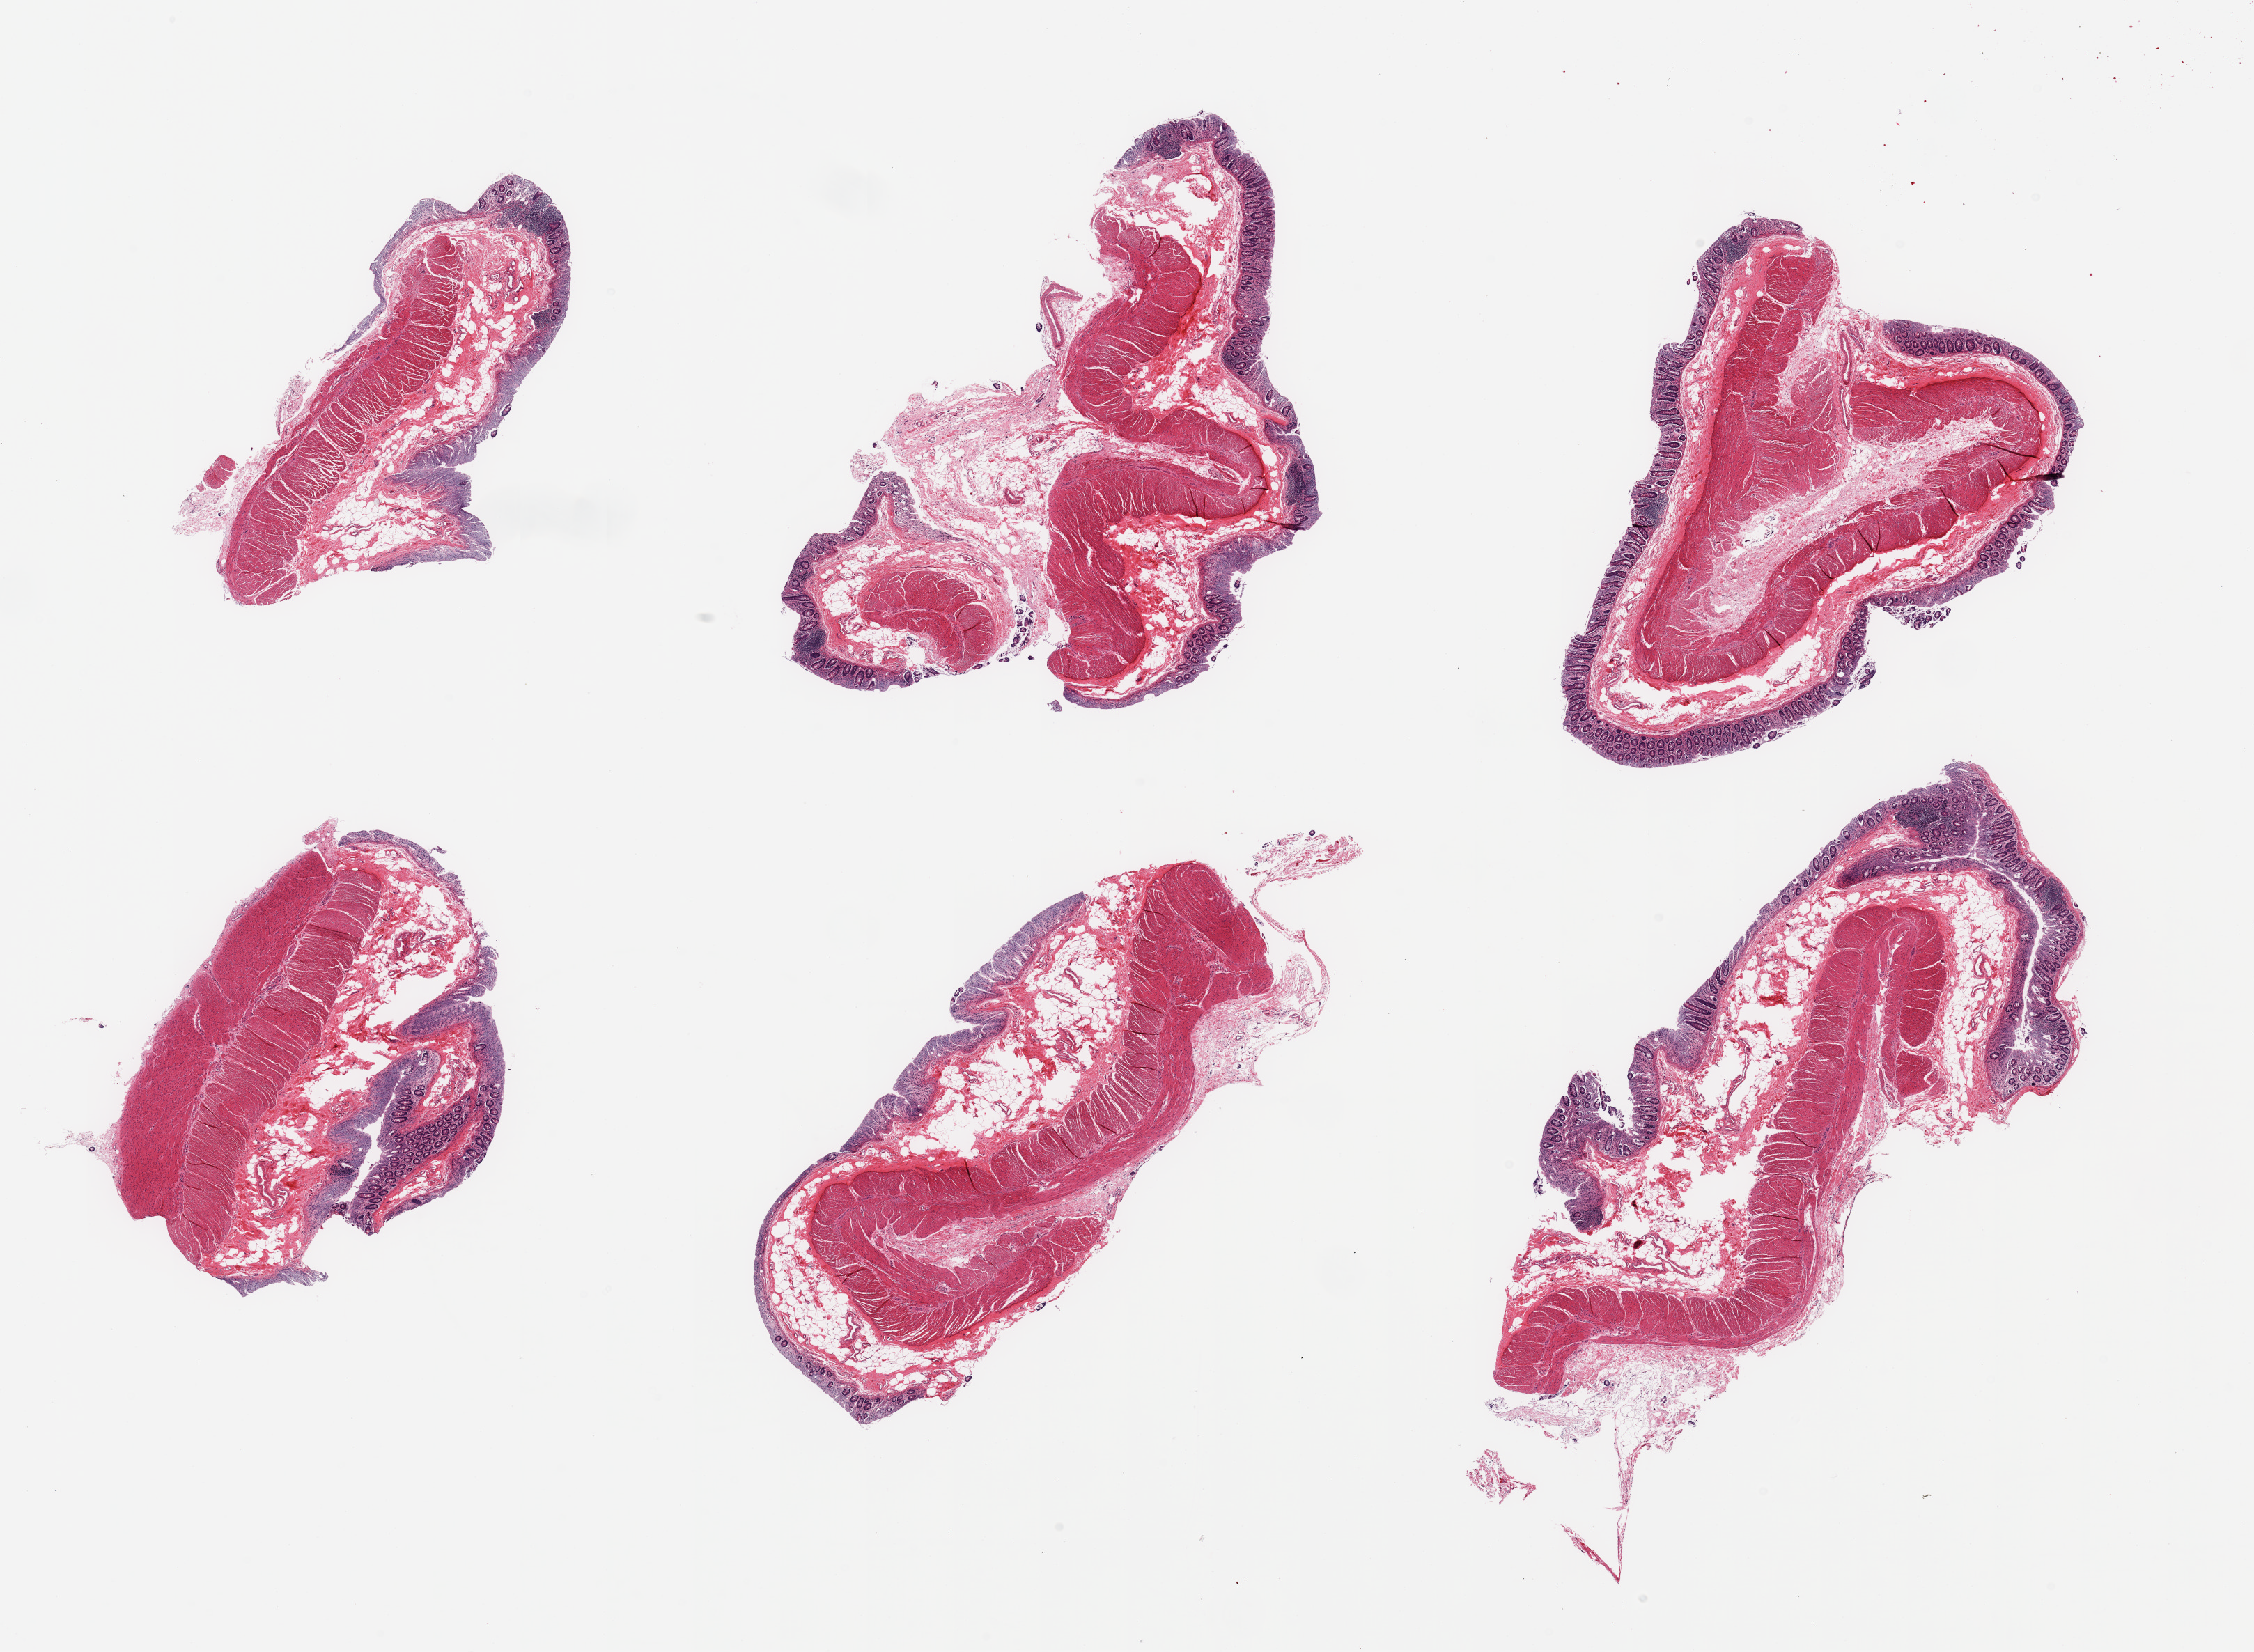
H&E whole-slide image, whole scanned area (about 25.6 x 18.8 mm, from a 20x scan) shown as a low-resolution overview, PAXgene-fixed paraffin-embedded (PFPE) section, section of transverse colon (target tissue), tissue donor sample.
* reviewer comment on this tissue sample: 6 pieces, mucosa is ~0.2-0.3mm, ~10% total thickness